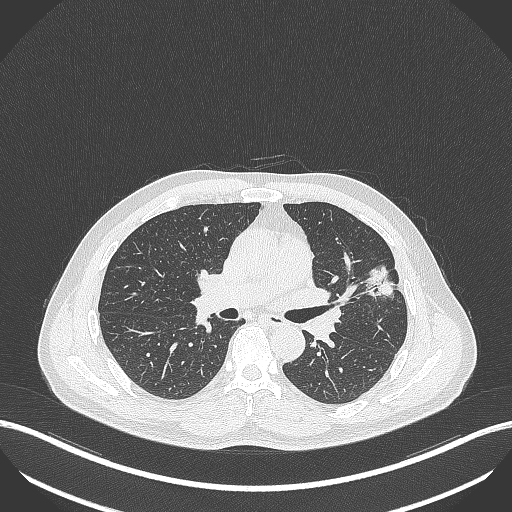
Chest CT, one axial slice; slice 227 of 418 in the series (ordered by position); lung window (W 1500 / L -600 HU); 1 mm slice thickness; 512 × 512 image matrix. Male patient, age 55 years. From the clinical record (not read from this slice): clinical TNM (as recorded): T1c N0 M0; histopathological grade: G2-3.
Structures marked on this image (bounding box drawn by a radiologist):
- lung tumour (recorded histology: adenocarcinoma): bounding box <364,265,399,302> (left, top, right, bottom; pixels)